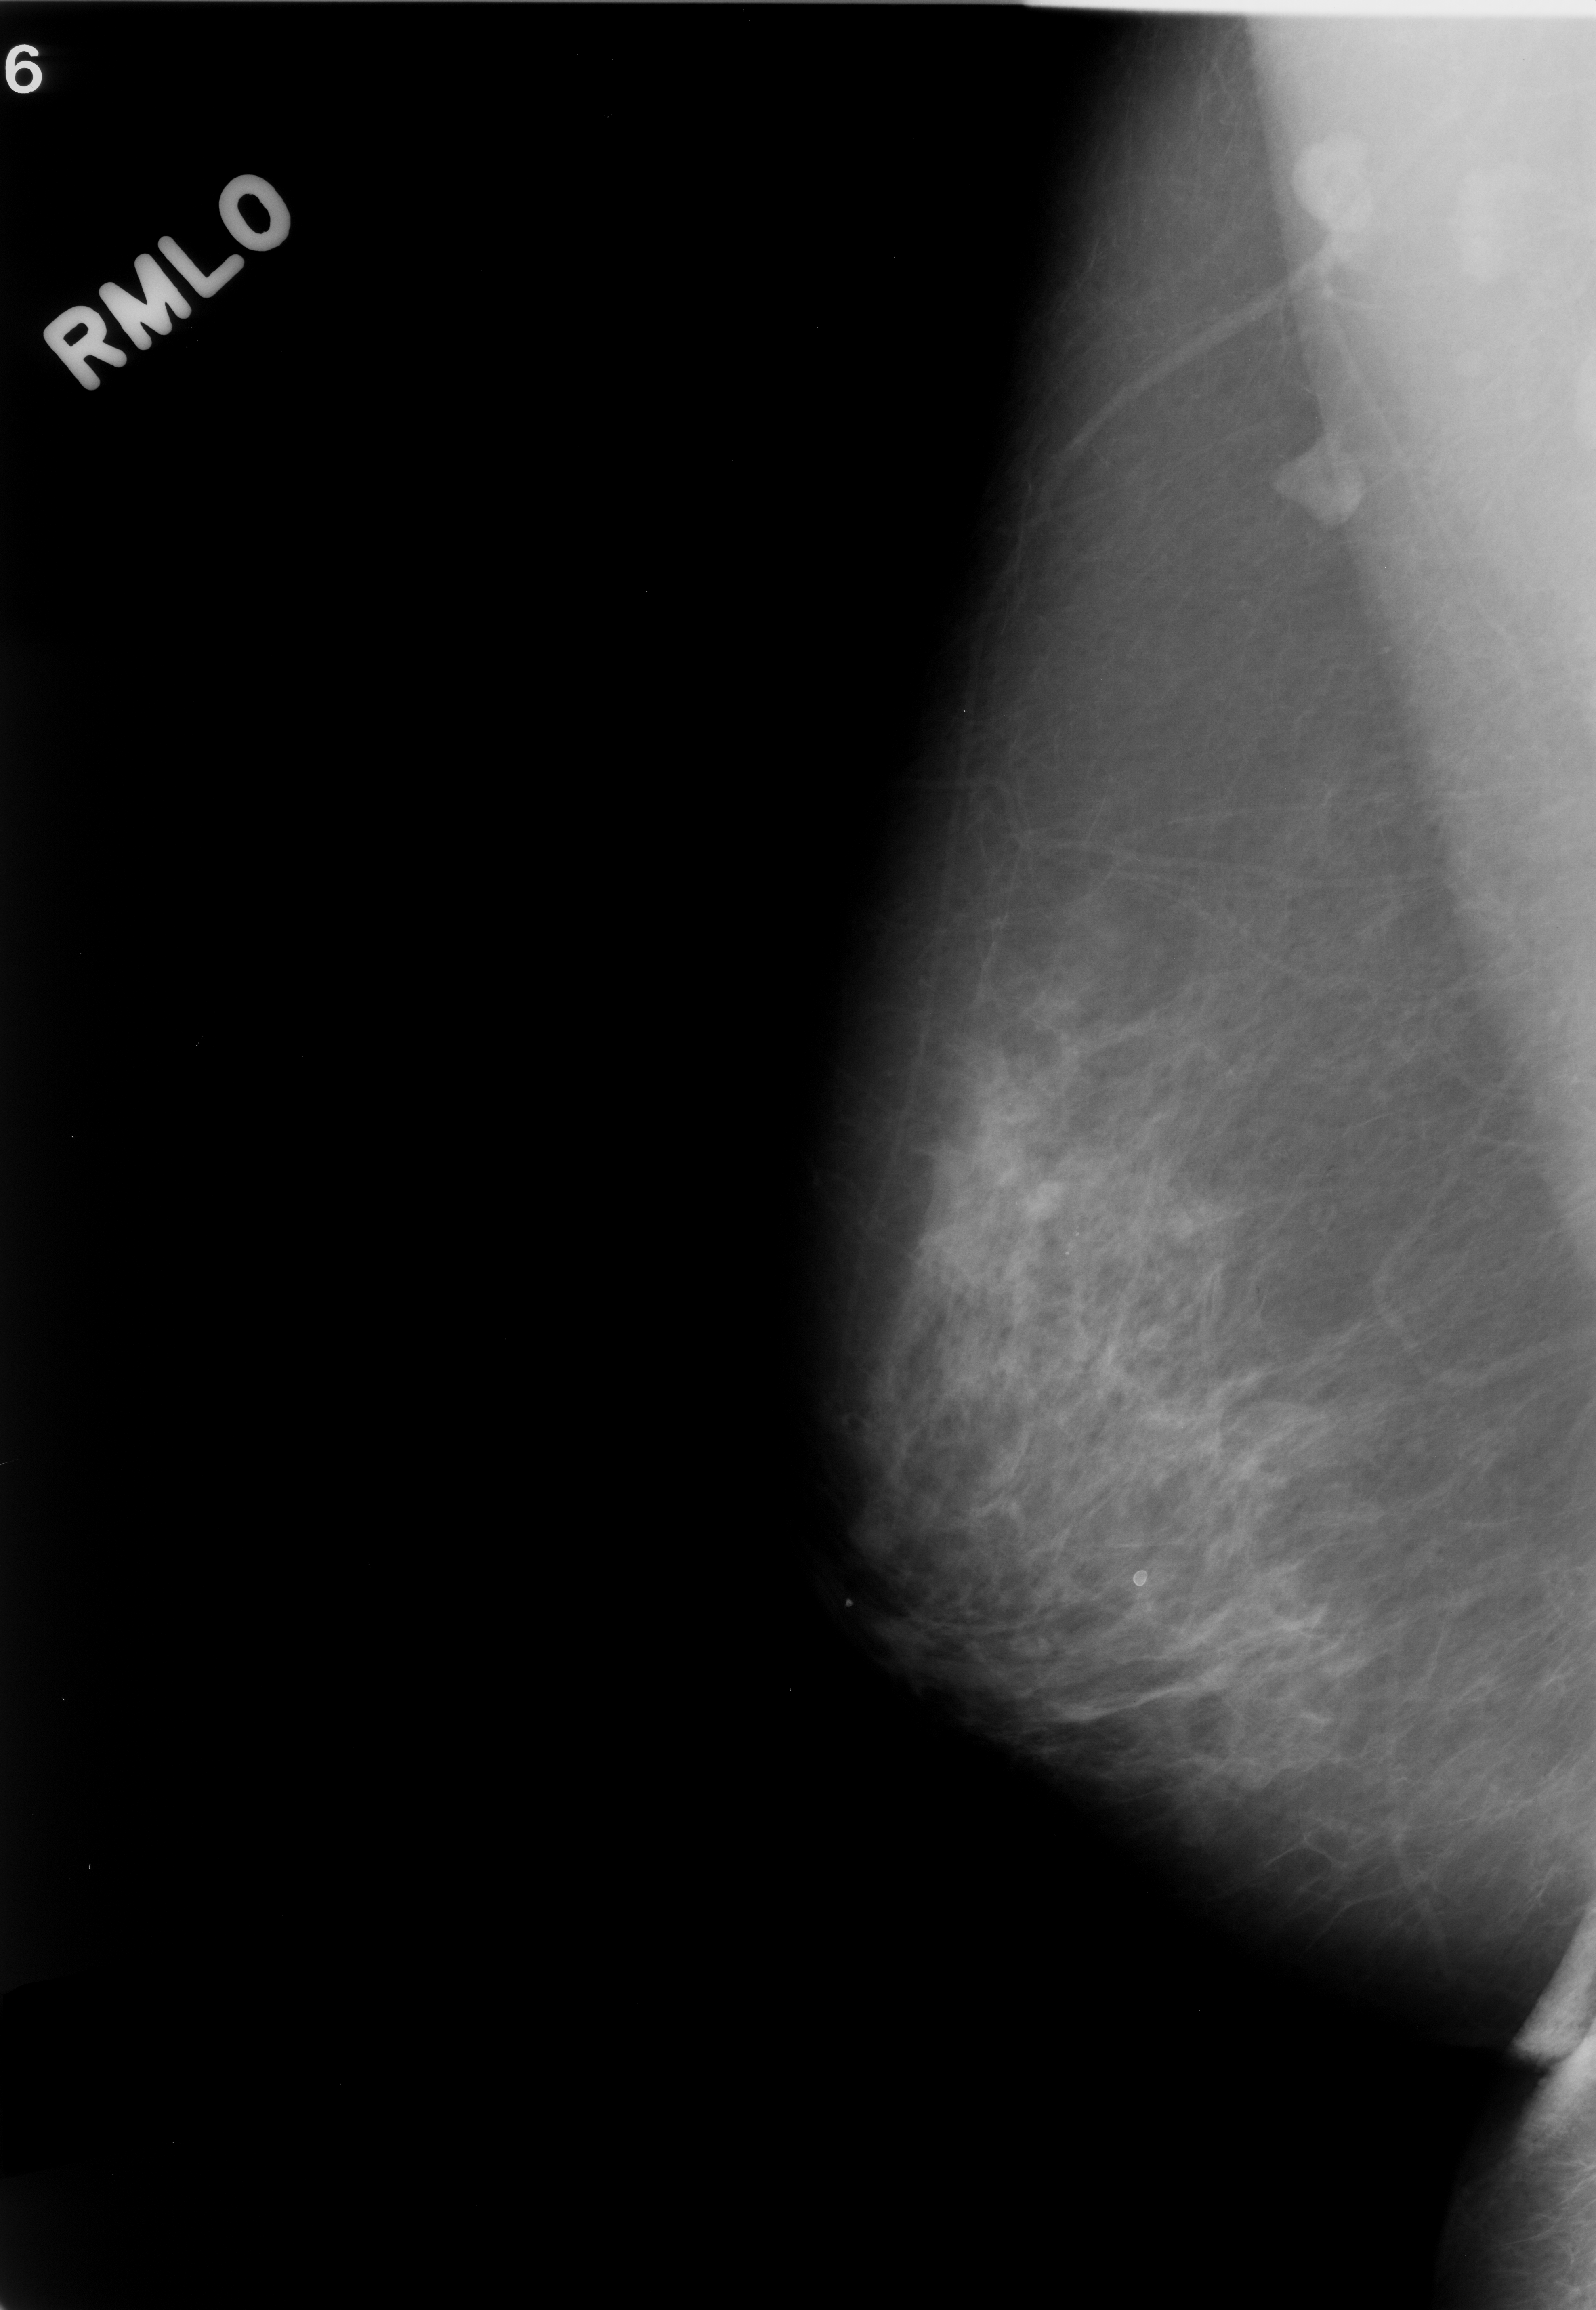
Mammogram (digitized film), right breast, MLO view, BI-RADS breast density category 2 (scale 1–4).
- Finding: calcifications, morphology pleomorphic, distribution clustered; BI-RADS assessment category 3; subtlety rating 3 on a 1 (subtle) to 5 (obvious) scale; pathology result (as recorded, not read from the image): benign.